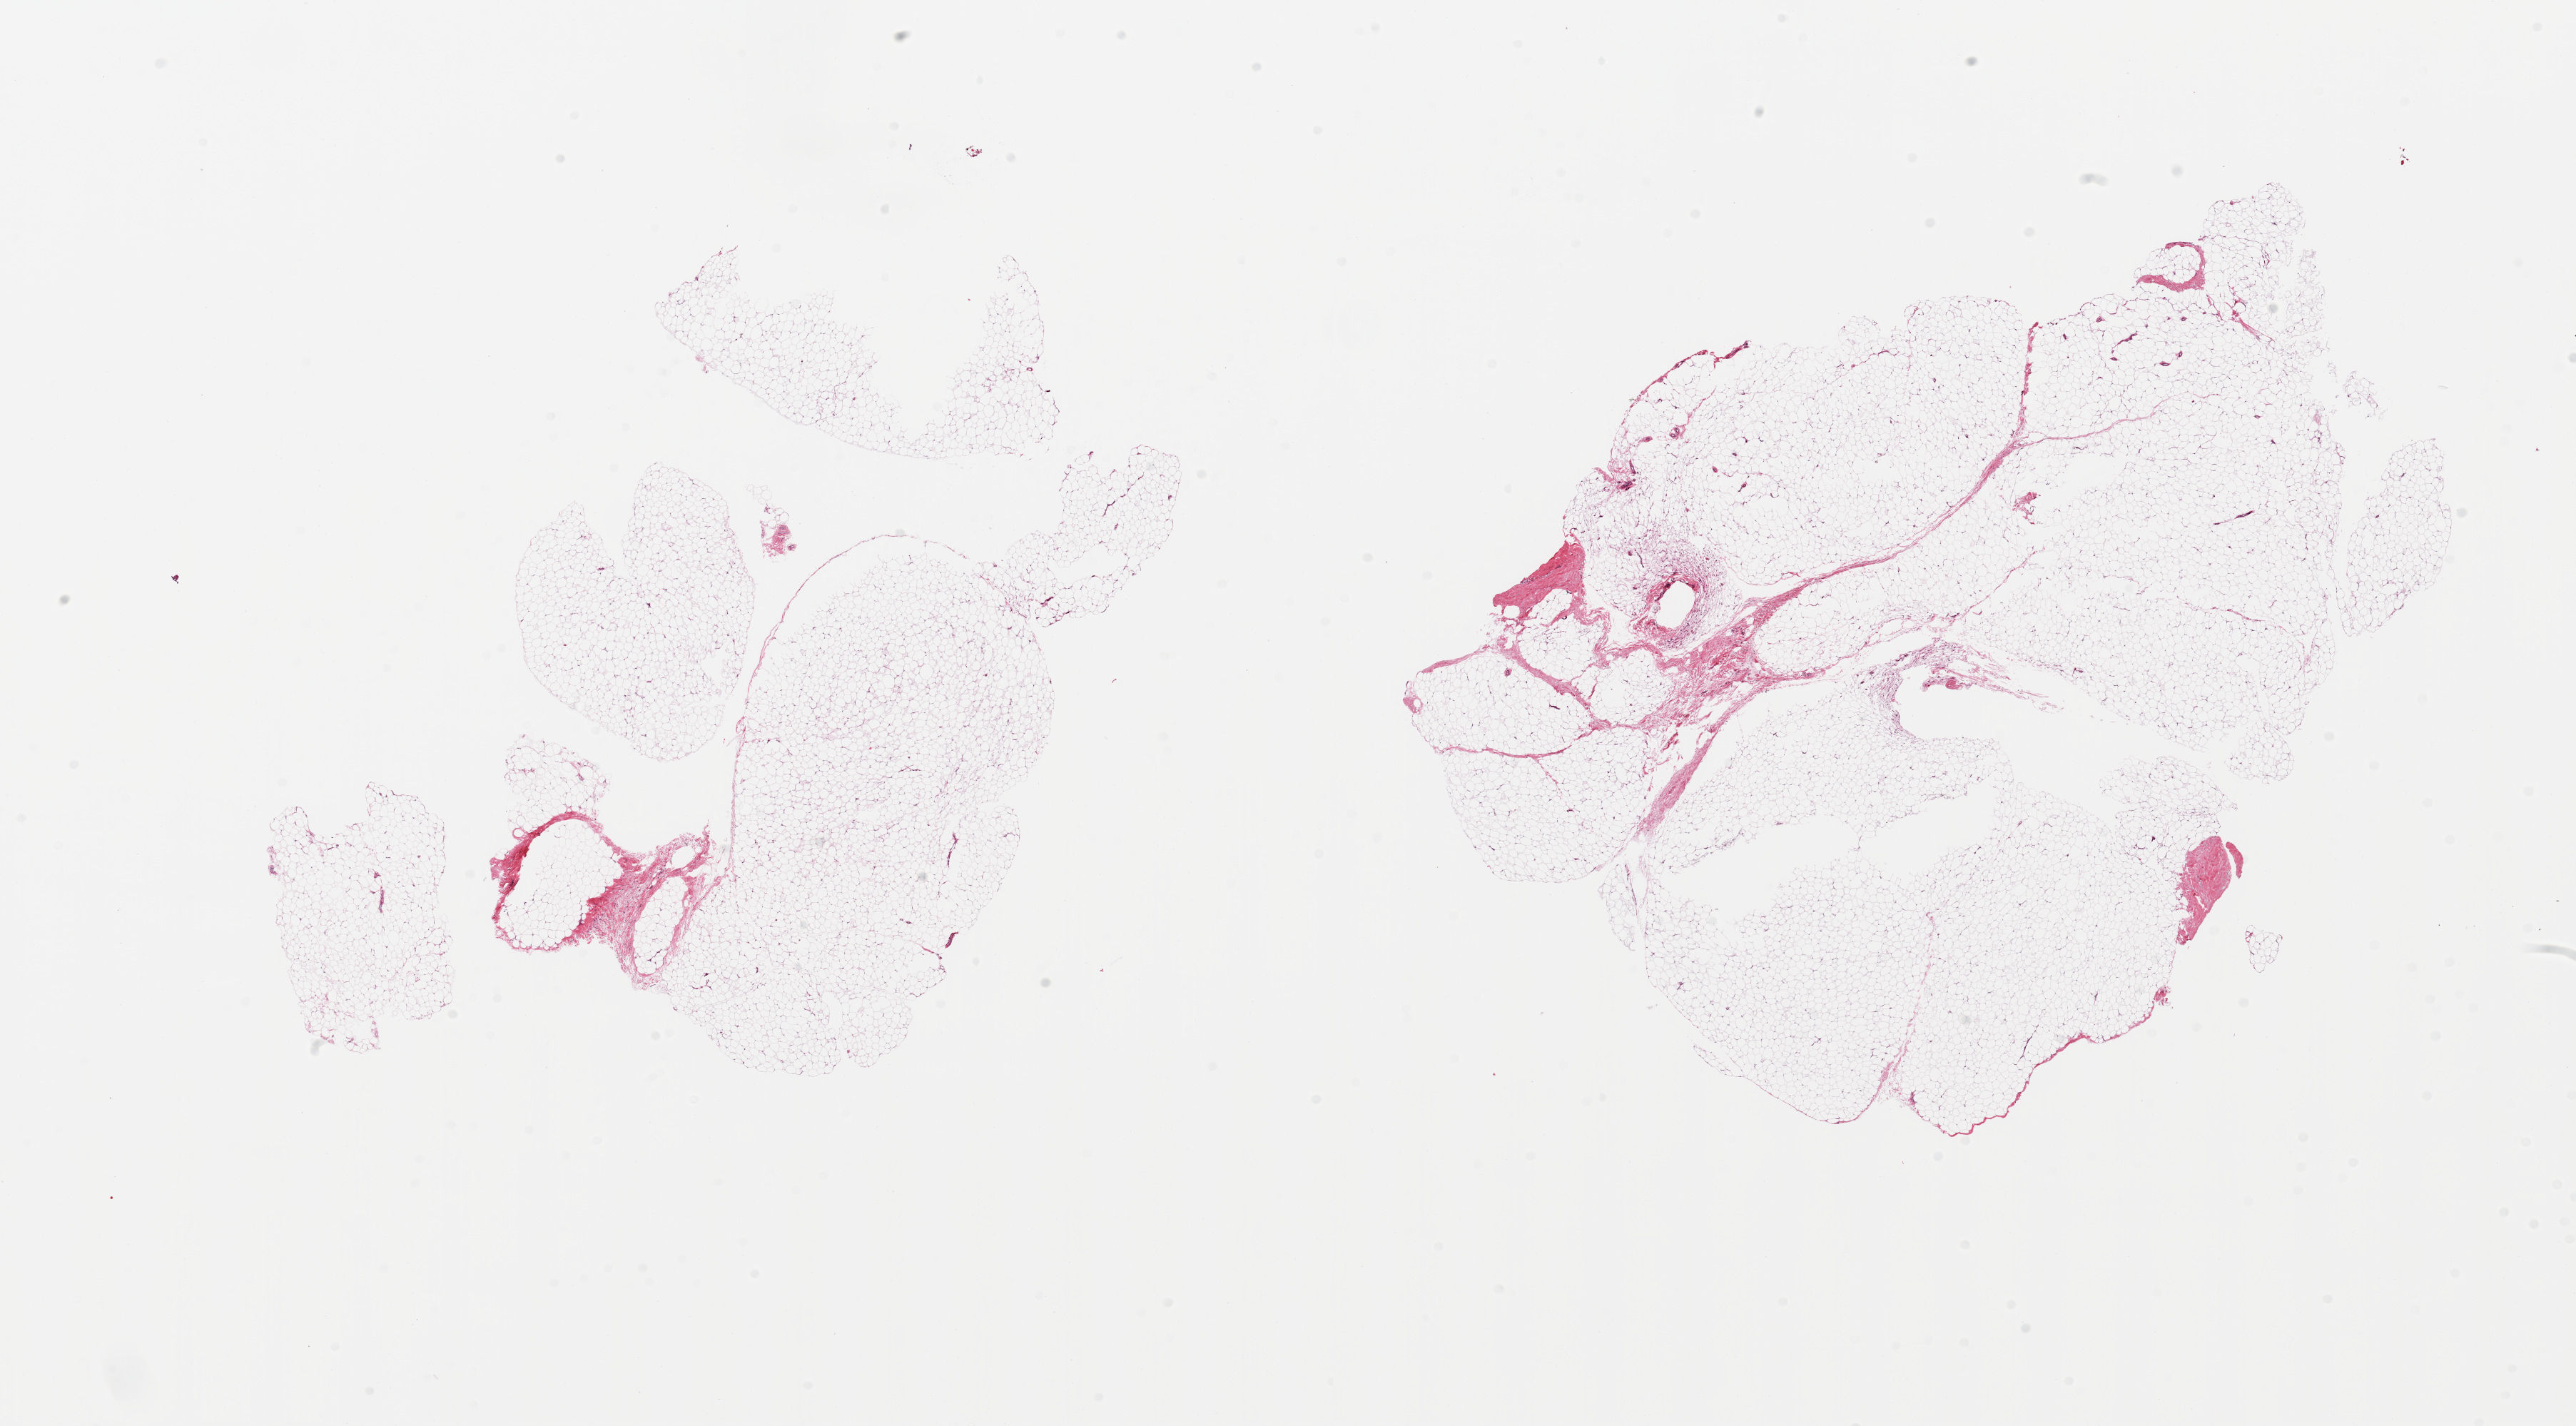
Whole-slide image, haematoxylin and eosin stain — low-resolution overview of the scanned area, about 28.5 x 15.8 mm. PAXgene-fixed paraffin-embedded (PFPE) section. Sampled site (target tissue): adipose tissue. Donor tissue sample. Female donor.
Review note (as recorded): 2 pieces, ~5-10% fascia/vascular elements.